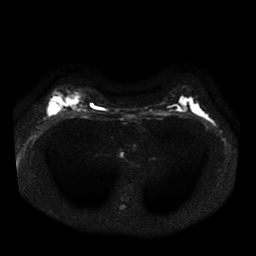
Breast MRI, one axial slice; position 25 of 41 along the scan axis; diffusion-weighted series; image 2 of 4 stored at this slice position (different b-values; order by instance number); 1.5 T; 256 × 256 image matrix, field of view 330 × 330 mm. Female patient.
Structures marked on this image (outlined manually by an expert reader):
- tumour on diffusion-weighted imaging: bounding box [x1, y1, x2, y2] px = [46, 101, 59, 113]